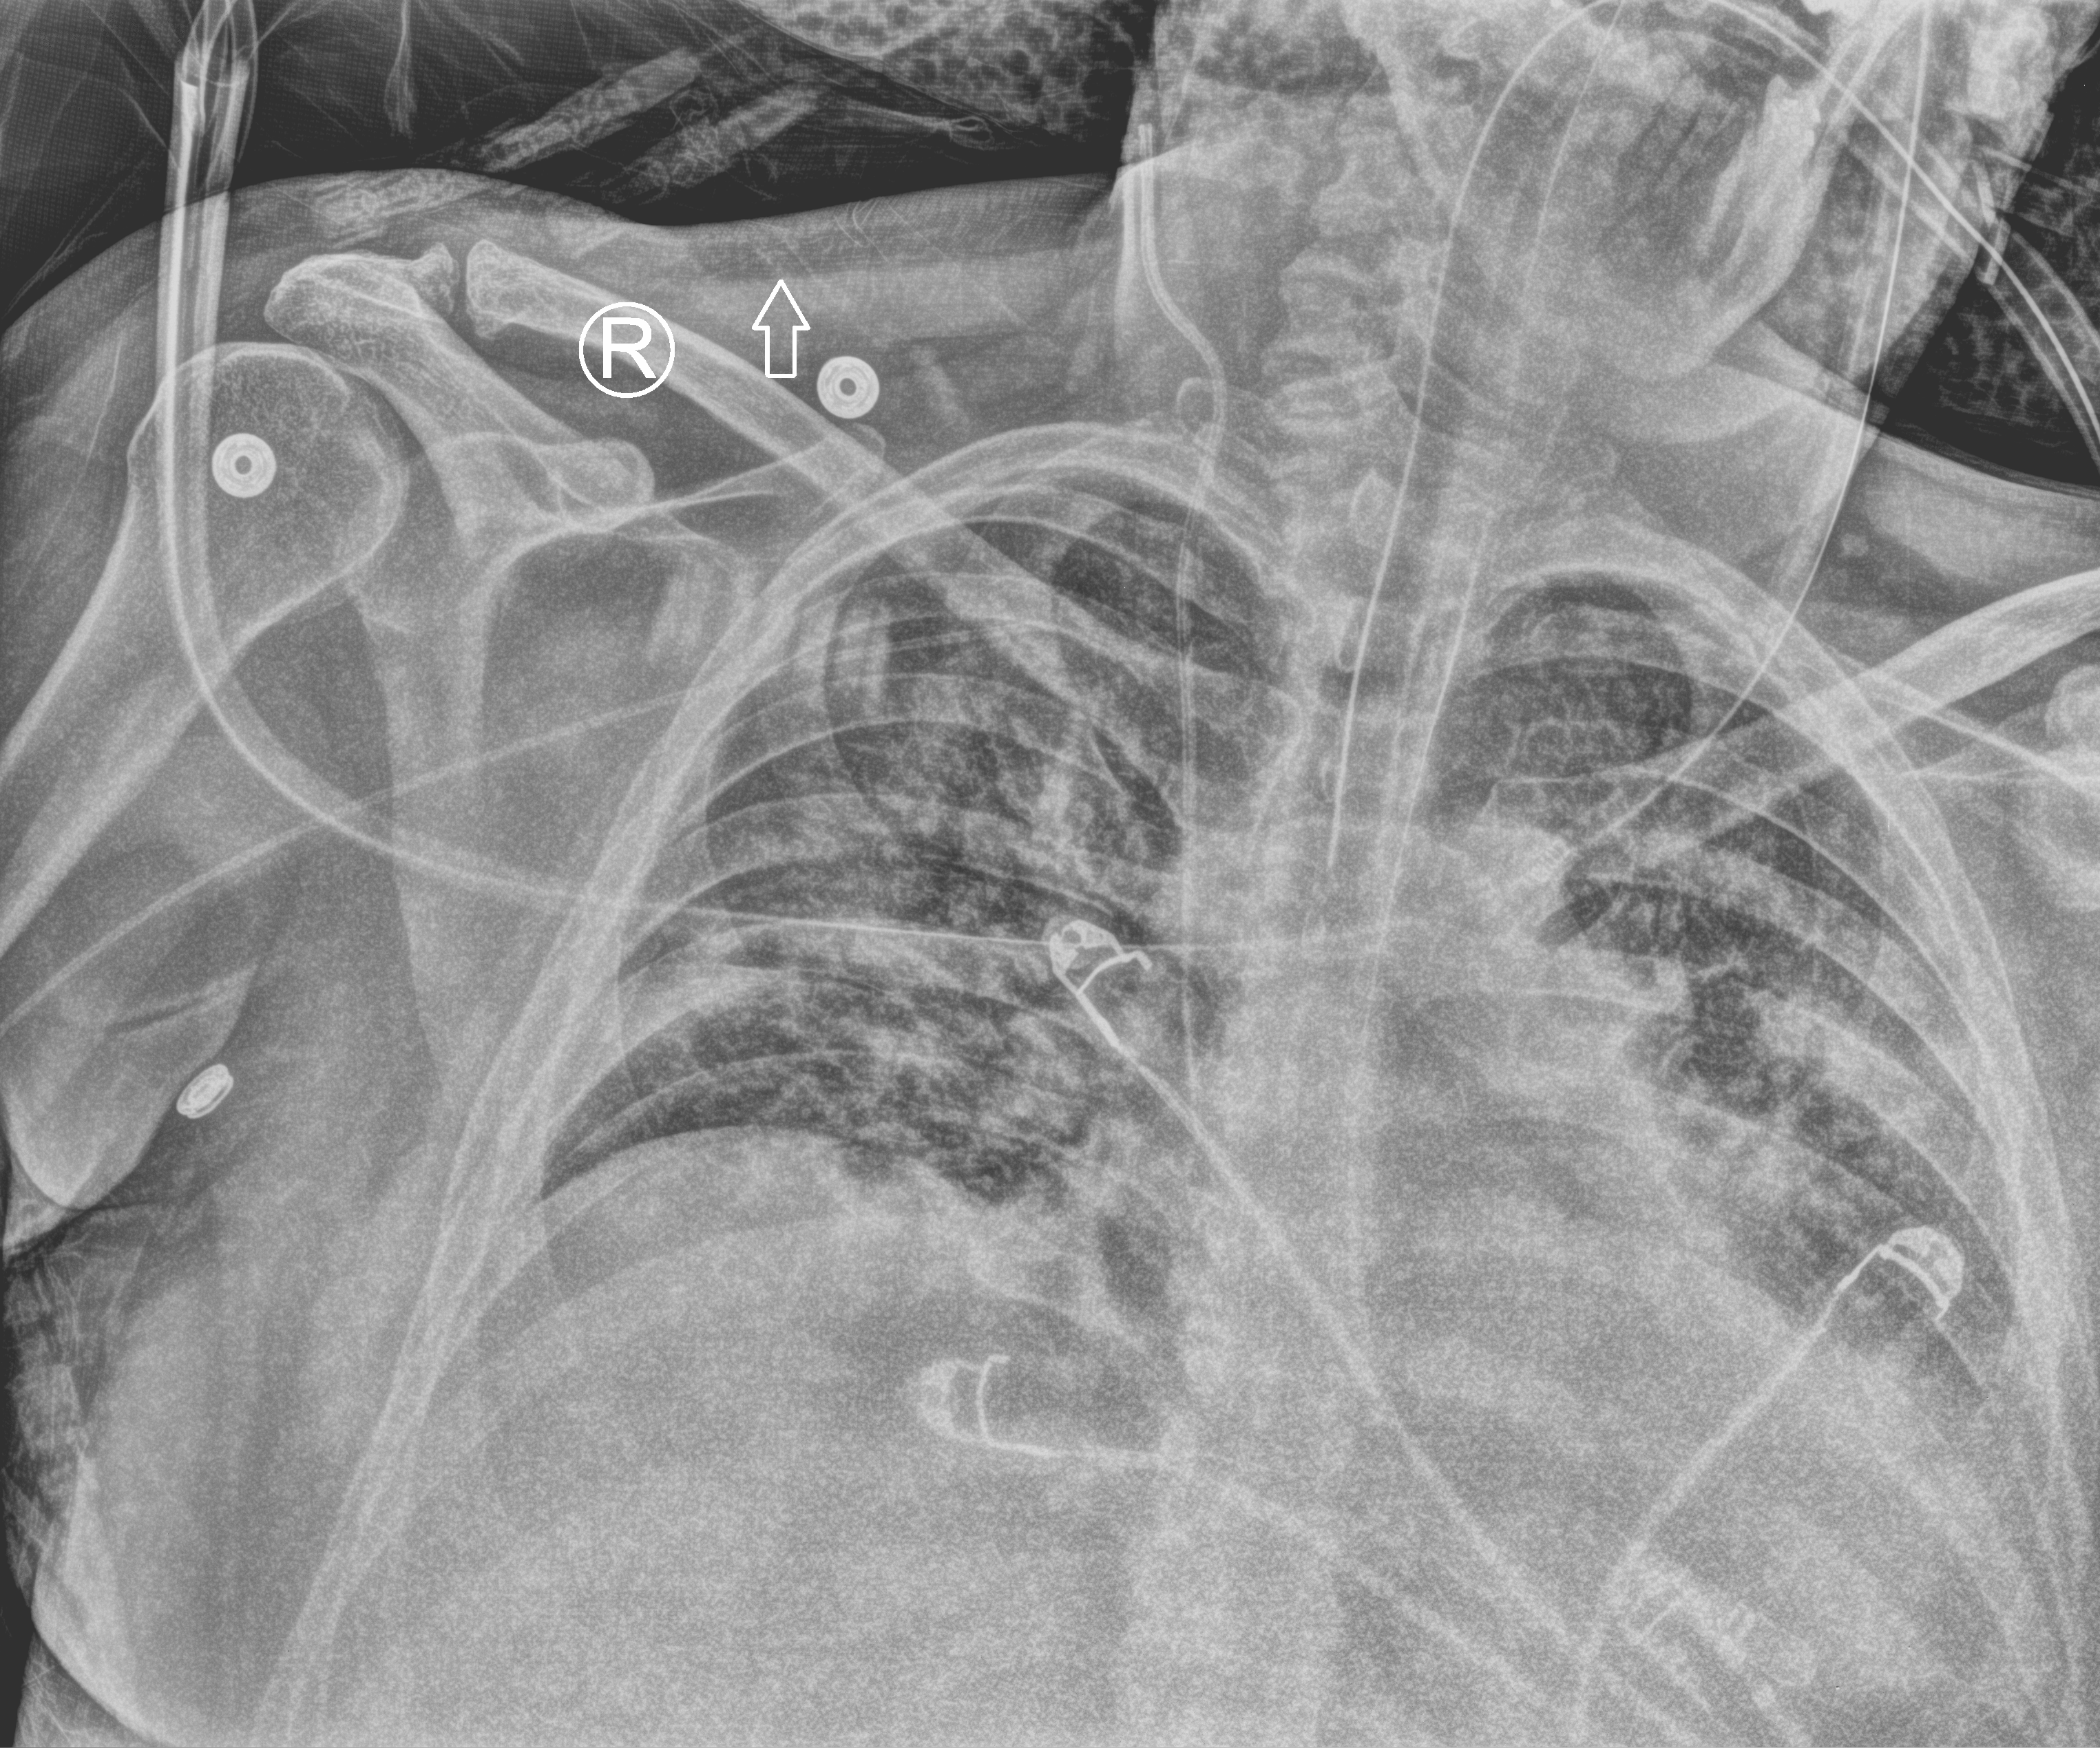
Chest X-ray (portable), anteroposterior (AP) projection. Patient hospitalised with COVID-19; male, aged 18–59 years.
Hospital-stay facts (about this admission, not read from this image; timing relative to this image not recorded): length of hospital stay: 39 days.